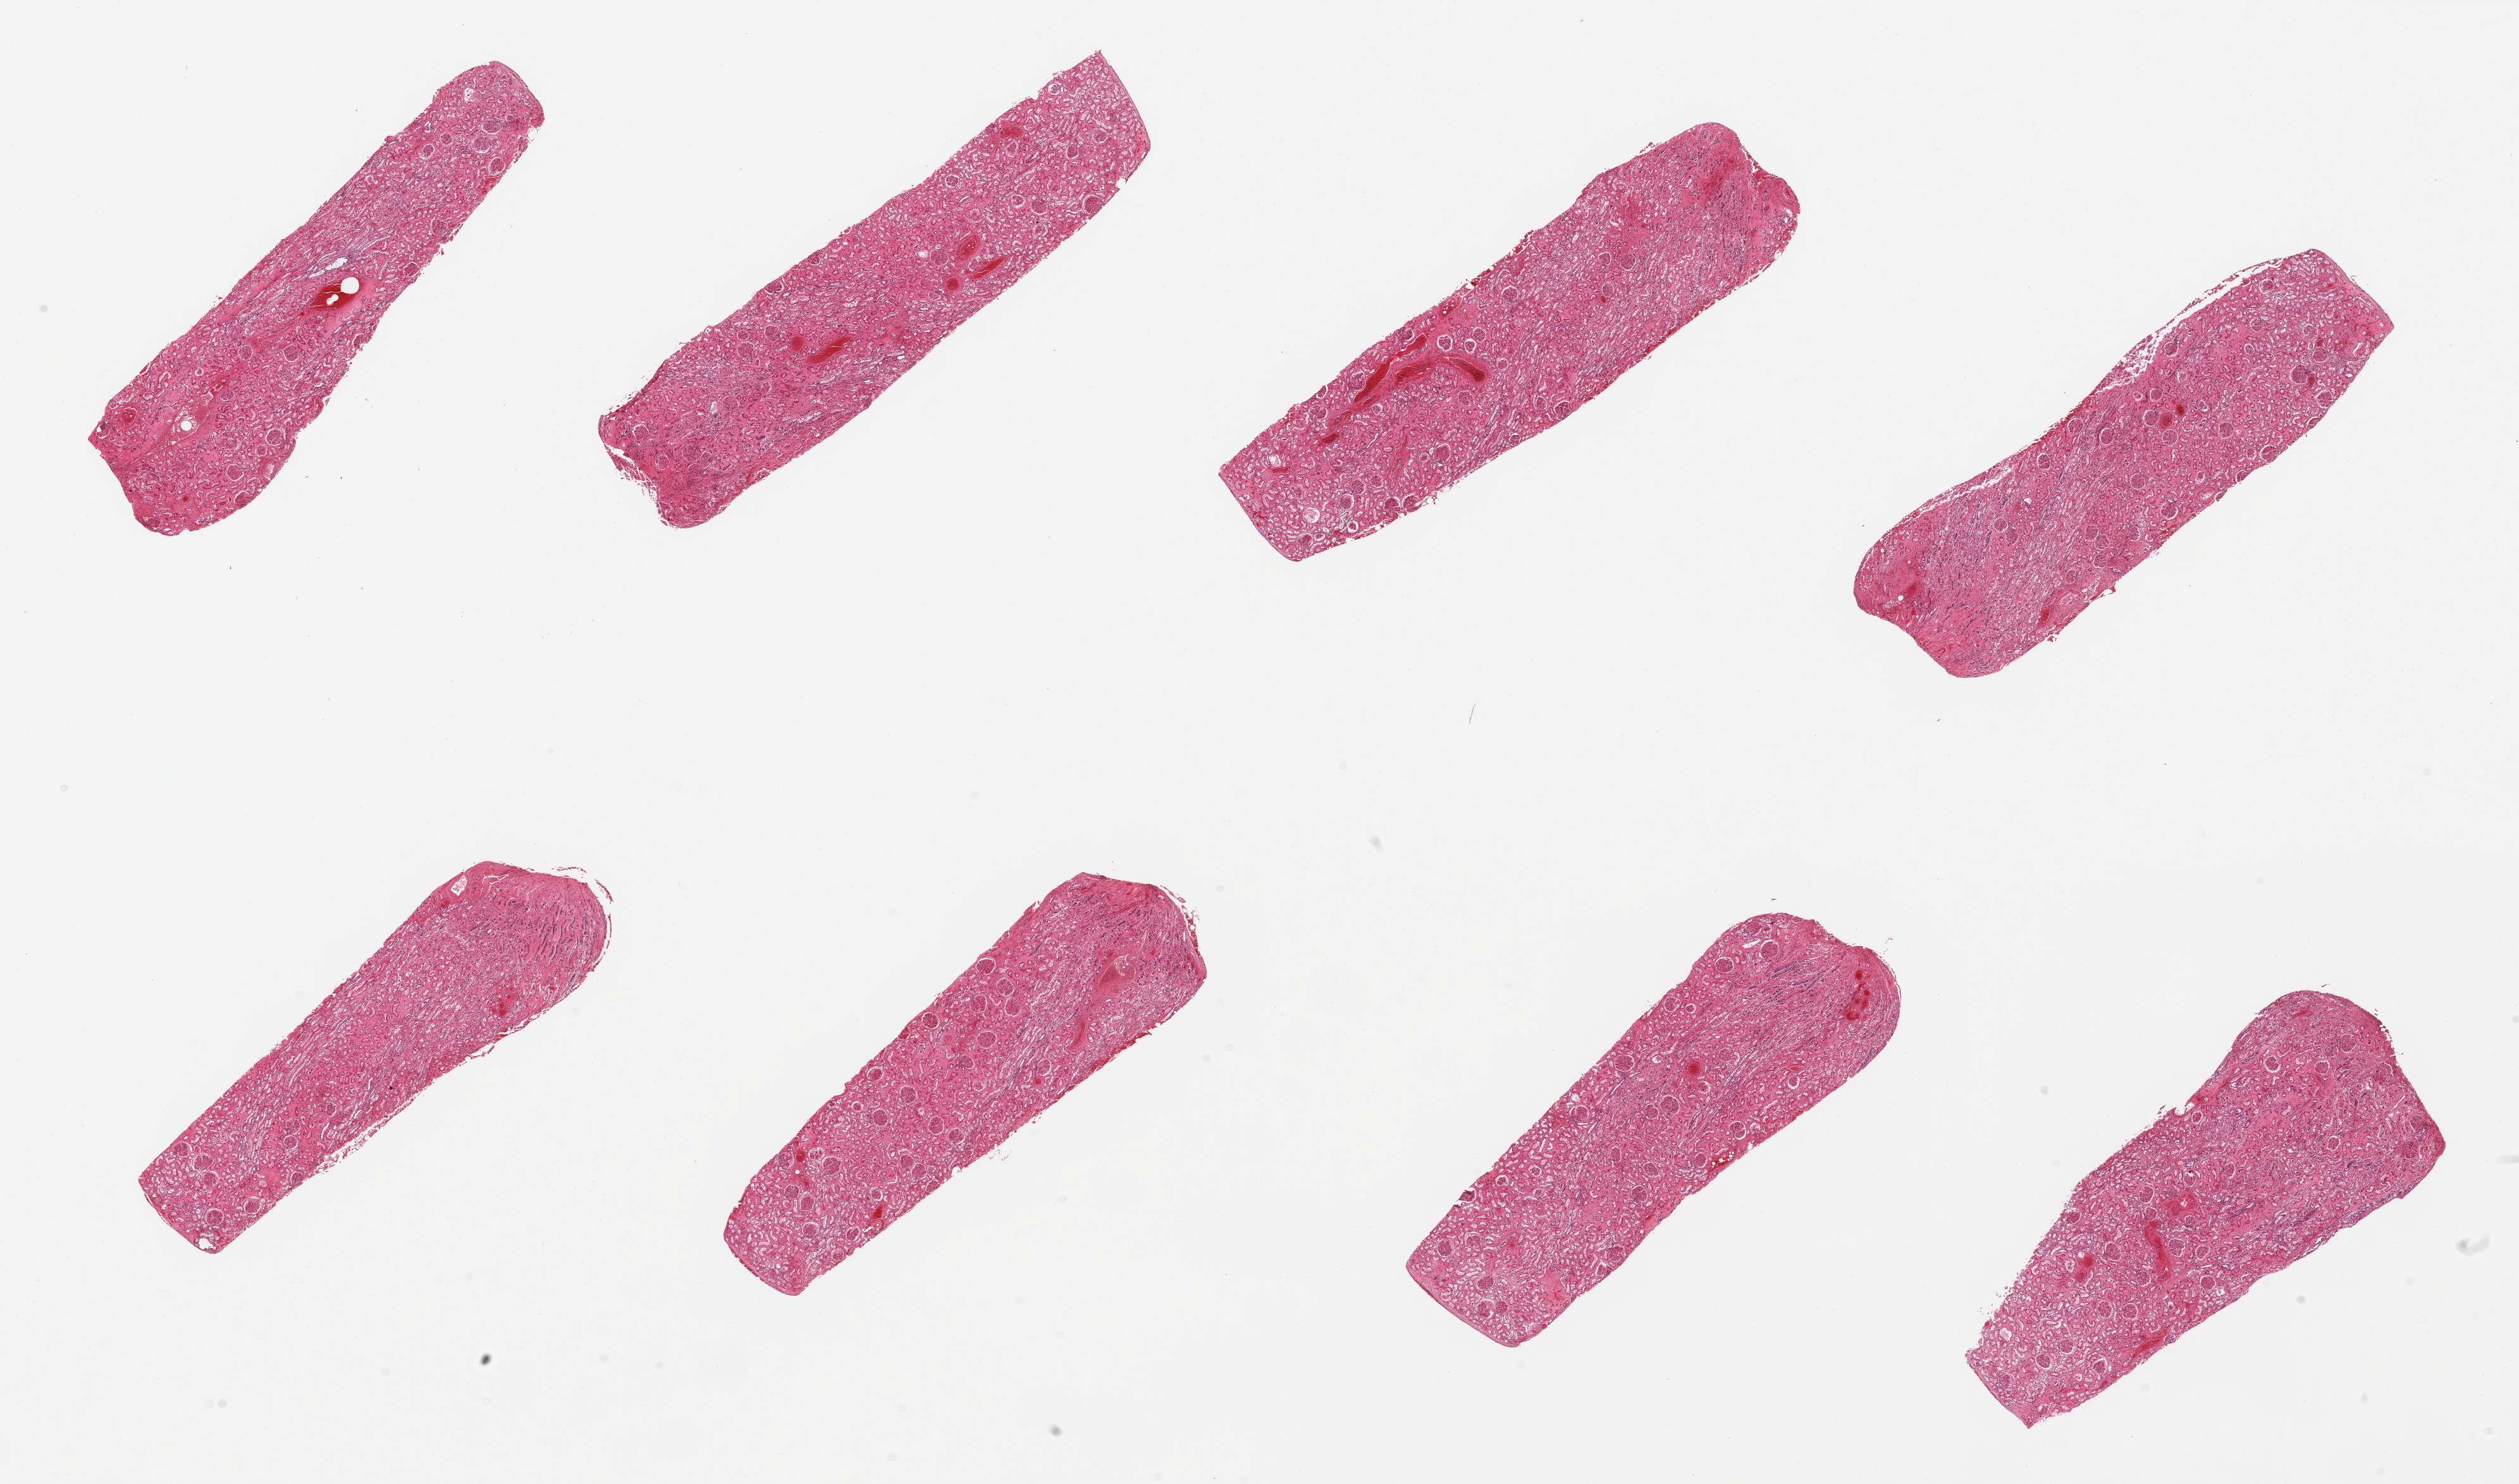
H&E whole-slide image — shown as a low-resolution overview of the whole scanned area (about 31.5 x 18.6 mm, slide scanned at 20x), PAXgene-fixed, paraffin-embedded tissue, section of renal cortex (target tissue), donor tissue sample. Male donor.
• reviewer comment on this tissue sample: 8 pieces; no lesions; 1 is 50% medulla